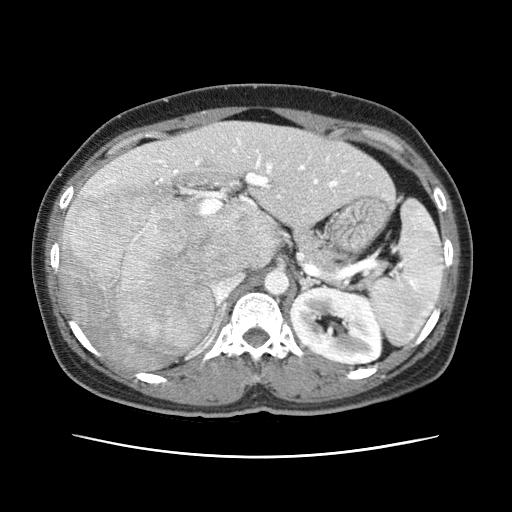
Contrast-enhanced abdominal CT (liver protocol), one axial slice. Slice 36 of 79 in the series (ordered by position). 120 kVp. Soft-tissue window (W 400 / L 40 HU). 2.5 mm slice thickness. 512 × 512 image matrix, field of view 340 × 340 mm. From the clinical record (not read from this slice): diagnosis: hepatocellular carcinoma (patient treated with transarterial chemoembolisation; whether this scan precedes or follows treatment is not stated here); TNM stage (as recorded): Stage-I; Child-Pugh class: A; tumour differentiation: moderately differentiated.
Structures marked on this image (semi-automatic segmentation, software-assisted and operator-edited):
- abdominal aorta: bounding box <264,269,289,294> (left, top, right, bottom; pixels)
- liver parenchyma outside the tumour (the mass and vessels are separate outlines, so this box may not span the whole liver): <60,121,394,370>
- mass: <62,182,227,370>
- liver vessels: <88,139,359,214>